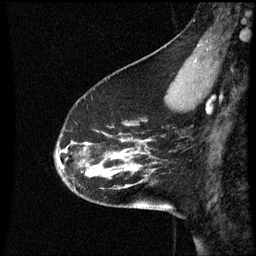
Breast MRI (dynamic contrast-enhanced), one sagittal slice. Position 15 of 60 along the scan axis. Dynamic contrast-enhanced series, image 2 of 3 at this slice position (ordered by acquisition). 1.5 T. TE 4.2 ms, TR 8.9 ms. 256 × 256 image matrix, field of view 200 × 200 mm. Female patient, age 45 years. Case-level facts recorded for this patient, not image findings: setting: breast cancer imaged before/during neoadjuvant chemotherapy; receptor status: HR-positive, HER2-negative.
Annotated regions visible in this slice (semi-automatically segmented with operator editing):
- analysis volume of interest (the breast-tissue region the enhancement analysis was run in; not a lesion): bounding box <54,94,171,205> (left, top, right, bottom; pixels)
- tumour enhancement mask (voxels above the 70 % enhancement threshold inside the analysis volume of interest): <56,142,129,173>